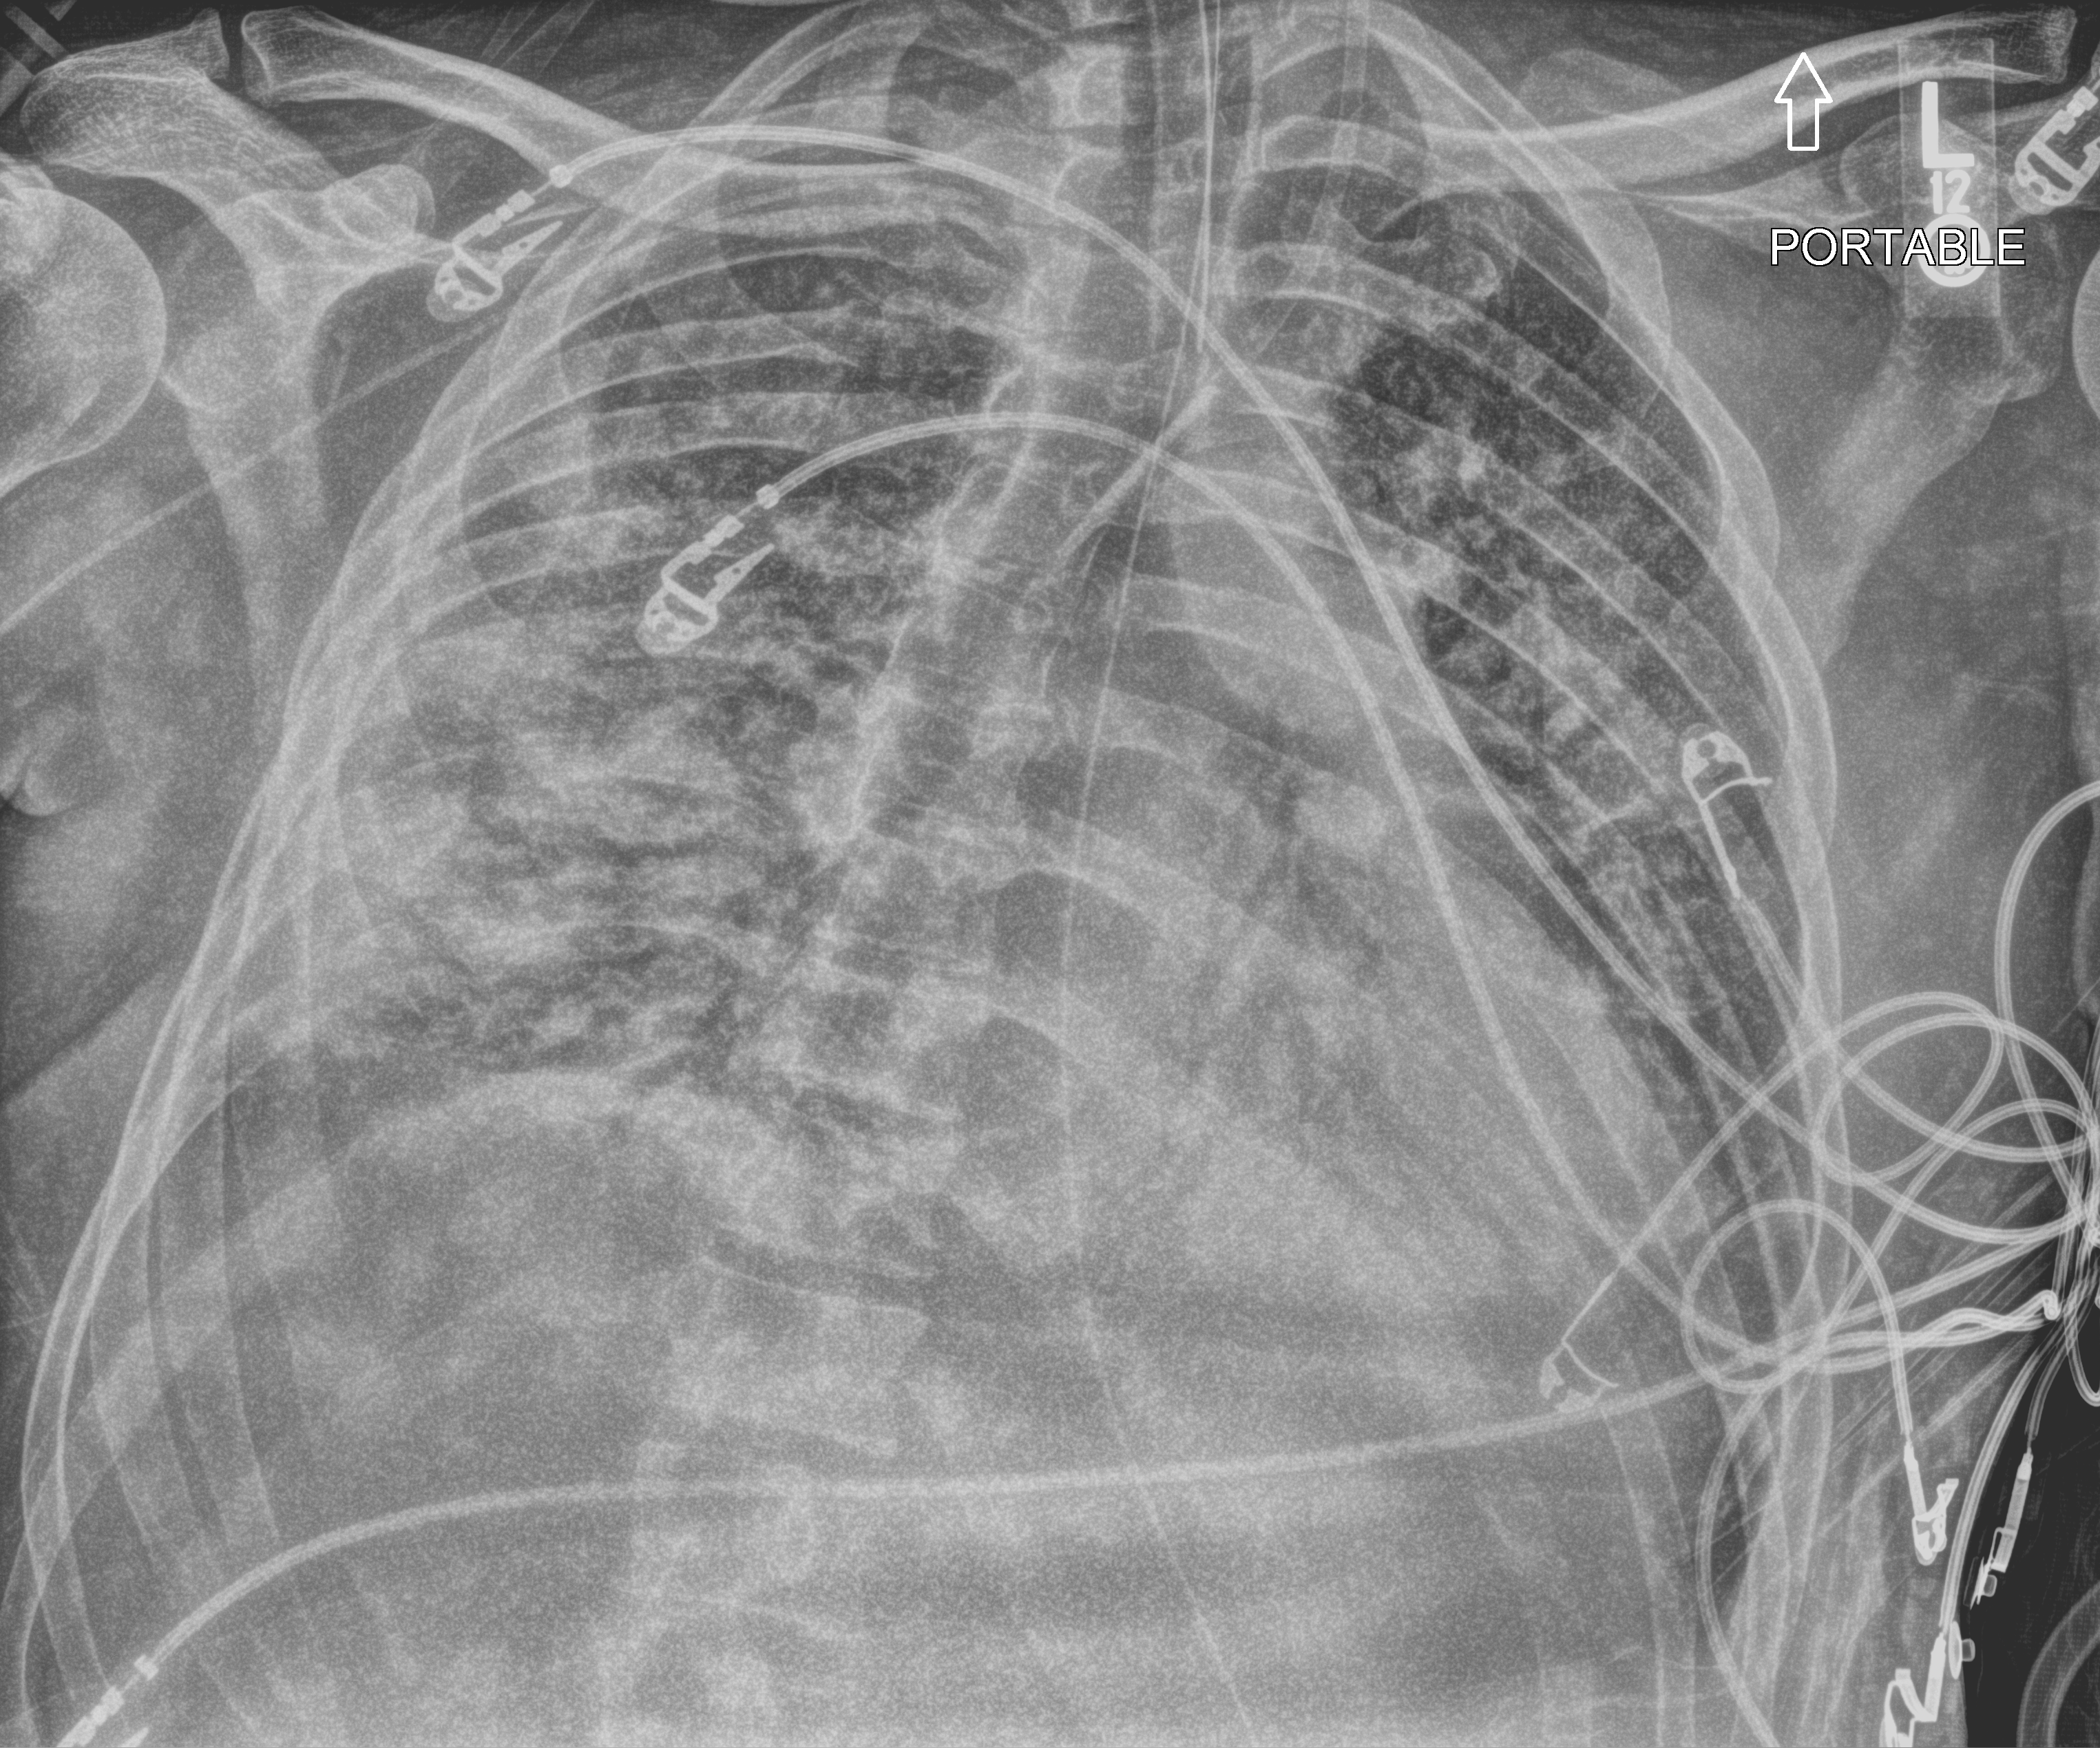
Chest X-ray (portable), anteroposterior (AP) projection. Patient hospitalised with COVID-19; male, aged 18–59 years.
From the hospital-stay record, not from the radiograph (when in the stay this image was taken is not recorded): admitted to intensive care during this hospital stay: yes; length of hospital stay: 75 days; hypertension (admission record): no.